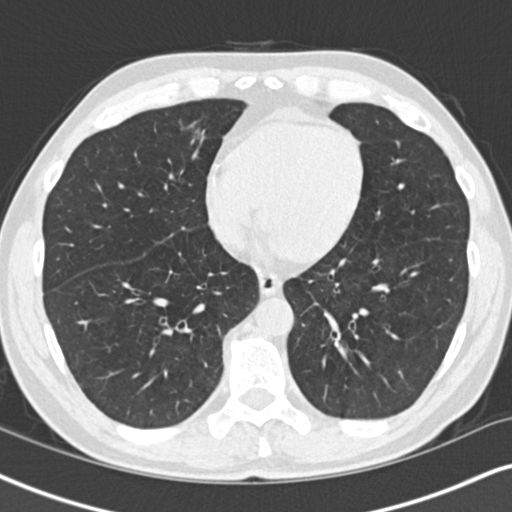
Low-dose screening chest CT, one axial slice; reconstruction kernel B30f; 120 kVp; lung window (W 1500 / L -600 HU); 512 × 512 image matrix, field of view 328 × 328 mm.
Structures marked on this image (outlined manually by an expert reader):
- lesion 1 (tumor, middle lobe of right lung): box from (x=196, y=130) to (x=199, y=133) px